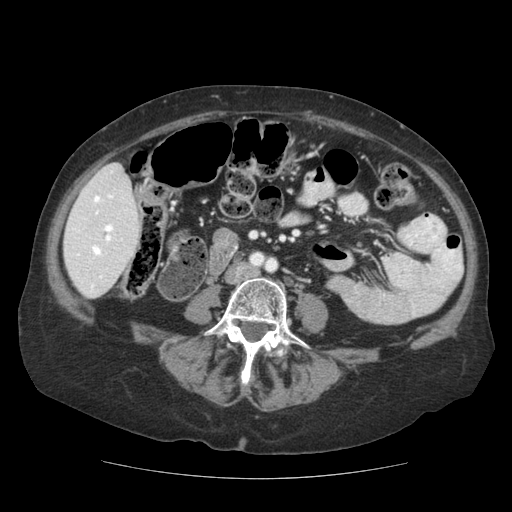
Contrast-enhanced abdominal CT (liver protocol), one axial slice. Position 33 of 111 along the scan axis. Reconstruction kernel STANDARD. 140 kVp. Soft-tissue window (W 400 / L 40 HU). 2.5 mm slice thickness. 512 × 512 image matrix, field of view 360 × 360 mm. From the clinical record (not read from this slice): diagnosis: hepatocellular carcinoma (patient treated with transarterial chemoembolisation; whether this scan precedes or follows treatment is not stated here); TNM stage (as recorded): Stage-I; Child-Pugh class: A; tumour differentiation: moderately-poorly differentiated.
Structures marked on this image (semi-automatically segmented with operator editing):
- liver parenchyma outside the tumour (the mass and vessels are separate outlines, so this box may not span the whole liver): bounding box (x1, y1, x2, y2) in pixels: (64, 163, 140, 298)
- liver vessels: (73, 194, 114, 290)